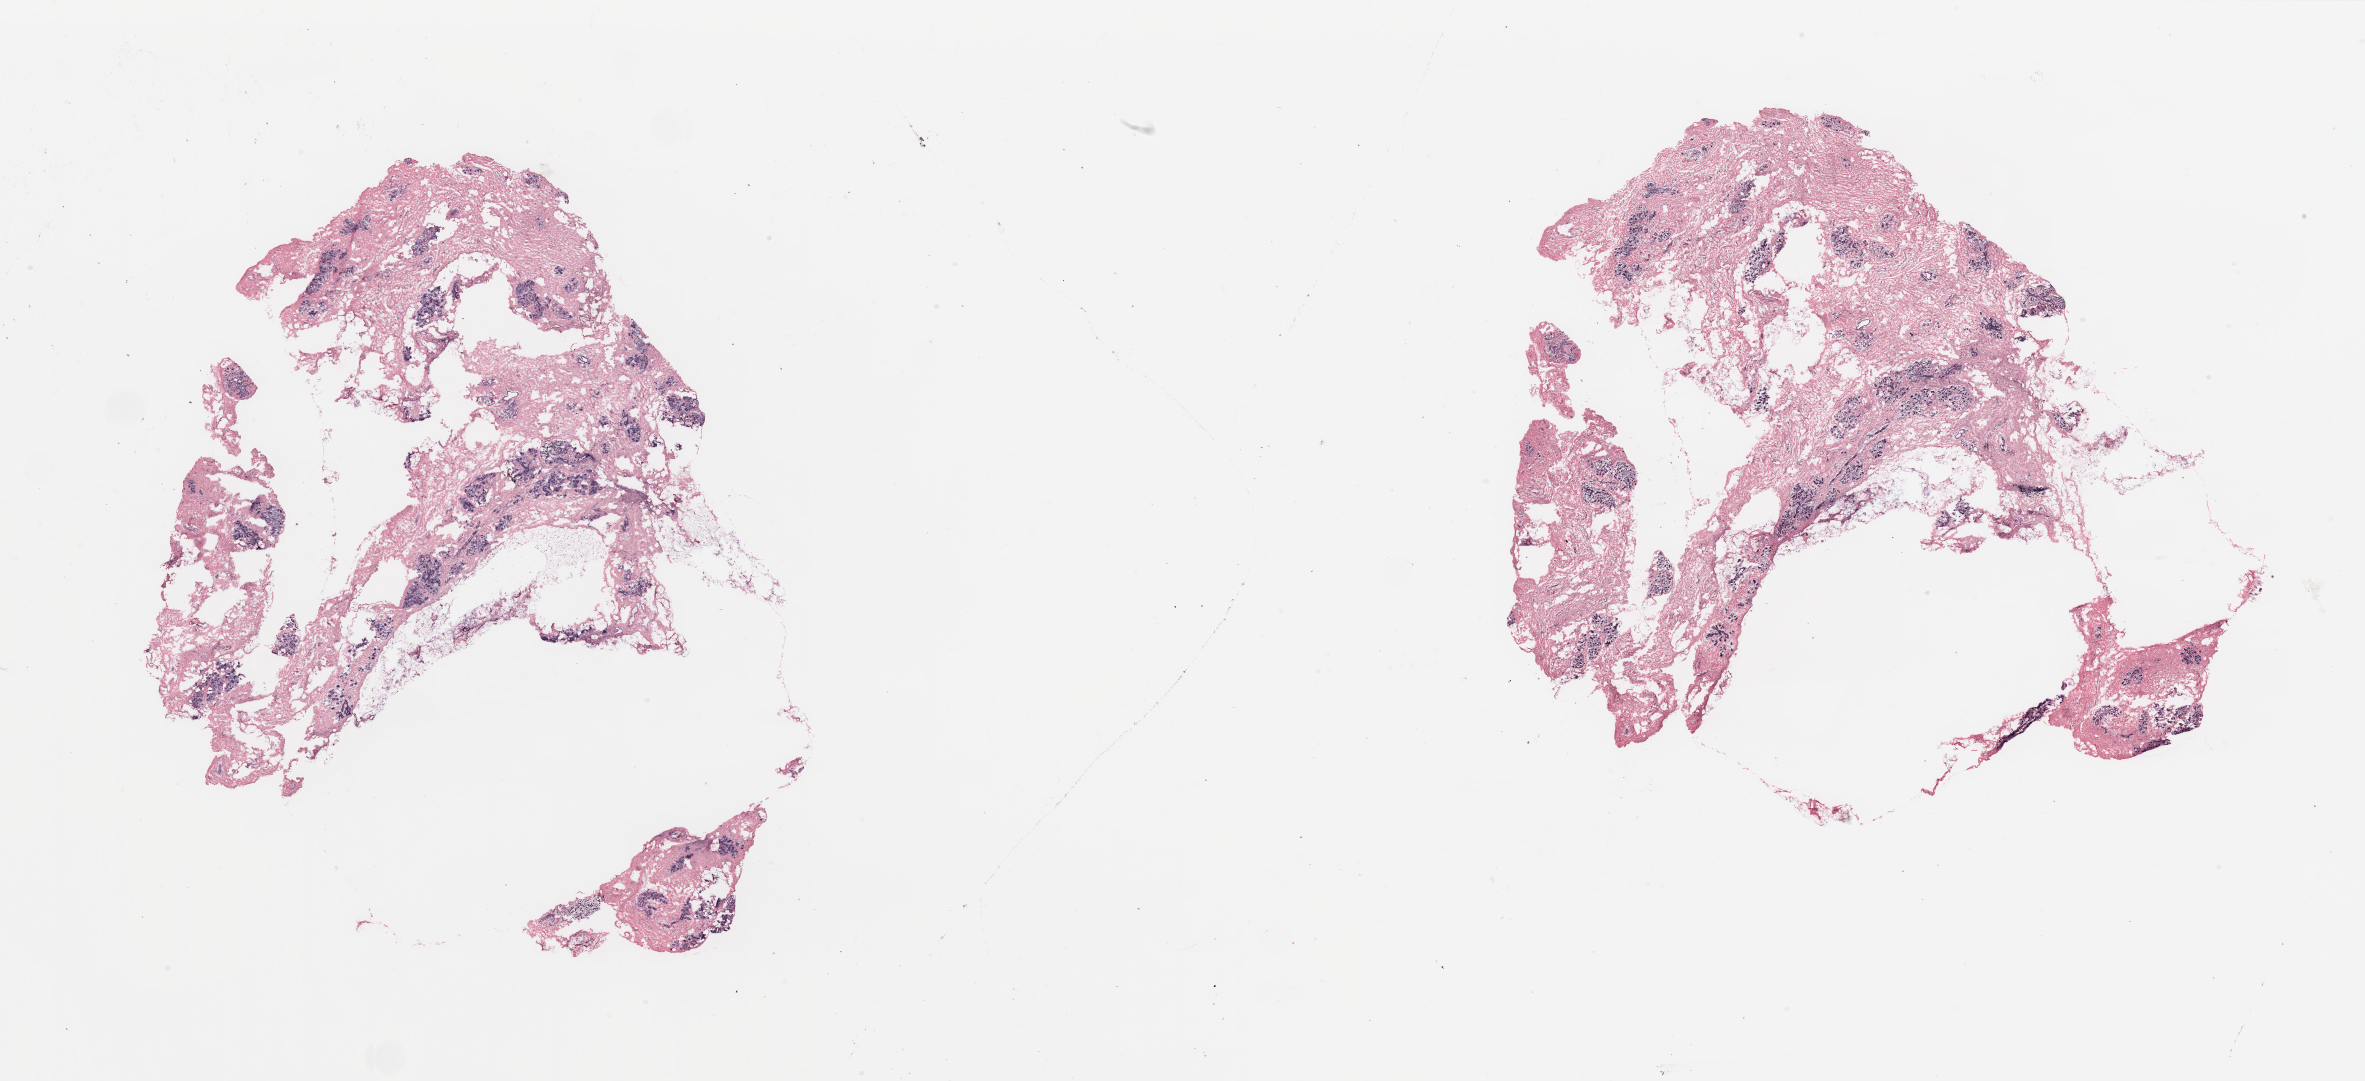
H&E whole-slide image — low-resolution overview of the scanned area, about 37.4 x 17.1 mm (from a 20x scan). Breast, tumour tissue. 55-year-old female patient.
AJCC pathologic stage: IIA. Diagnosis: Infiltrating duct carcinoma, NOS.